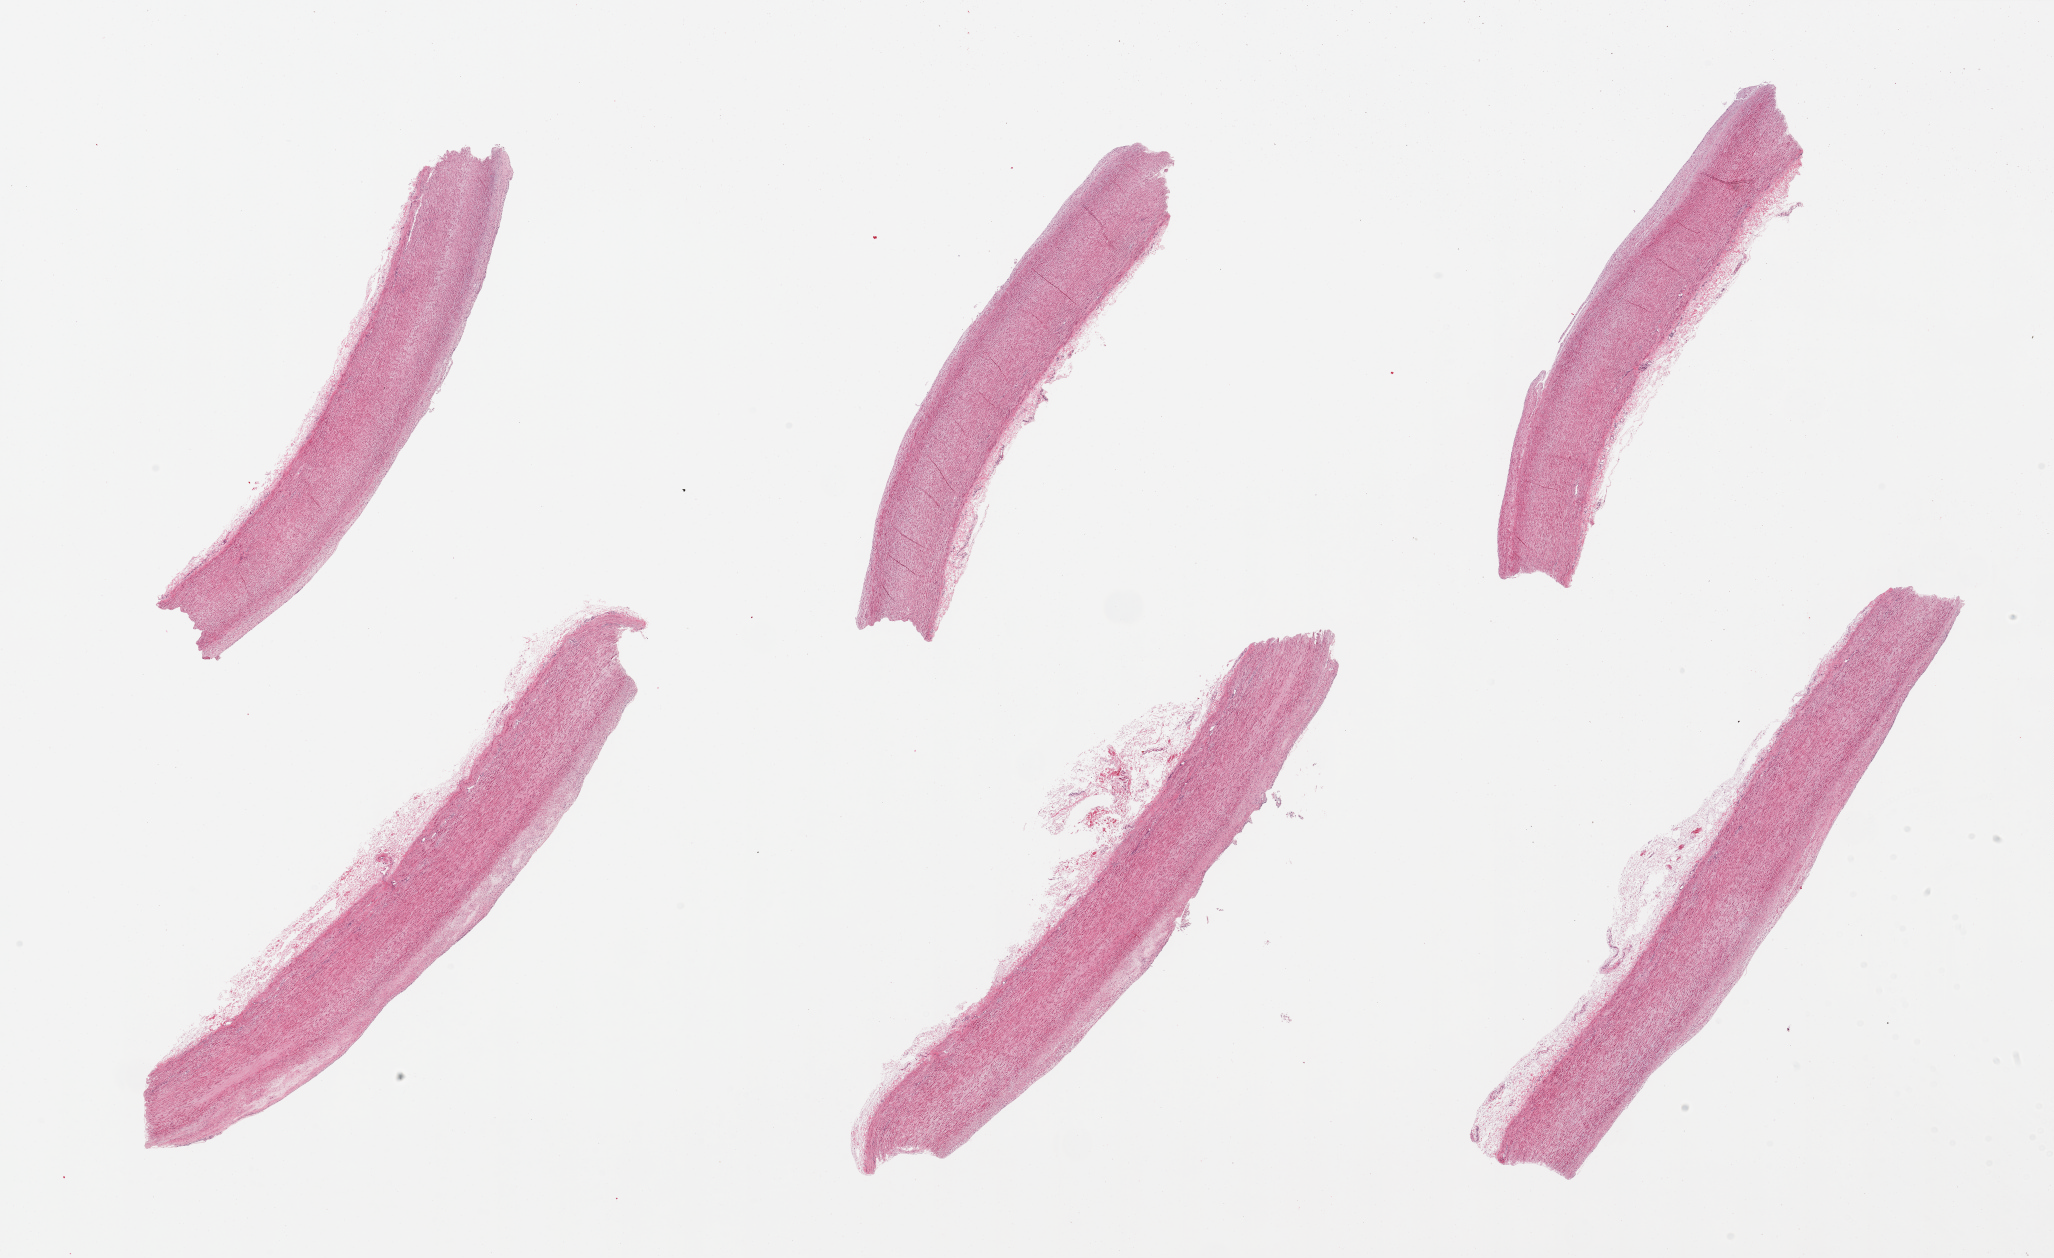
Digitized H&E-stained section, brightfield, a low-resolution overview of the entire scanned area, about 32.5 x 19.9 mm; PAXgene-fixed paraffin-embedded (PFPE) section; sampled site (target tissue): aorta; tissue donor sample. Donor sex: female.
- pathologist's review note for this sample: 6 pieces, intimal thickening